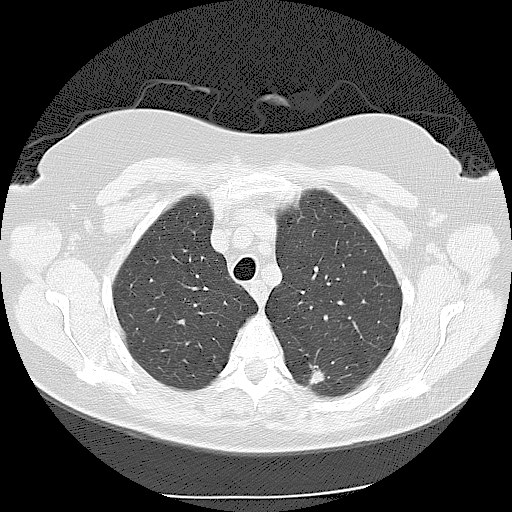
Chest CT (low-dose screening protocol), one axial image; second annual screen; lung window (W 1500 / L -600 HU); 2.5 mm slice thickness; slice 28 of 116 in the series. Female participant, aged 56 years at enrolment. Current smoker at enrolment.
Expert reader's lesion annotation, bounding box (x1, y1, x2, y2) in pixels: (290, 347, 348, 402). The exam's reader record, not a measurement of the box and not confirmed to be the same lesion: non-calcified nodule or mass ≥4 mm, left lower lobe, 9 × 9 mm, spiculated (stellate) margins, soft tissue attenuation, pre-existing on the prior screen: yes; interval growth: yes. Official screen result: positive, other. Lung cancer was diagnosed 173 days after this screen: adenocarcinoma, NOS, left lower lobe, moderately differentiated (G2), stage IIA (AJCC 6th edition), 15 mm at pathology.